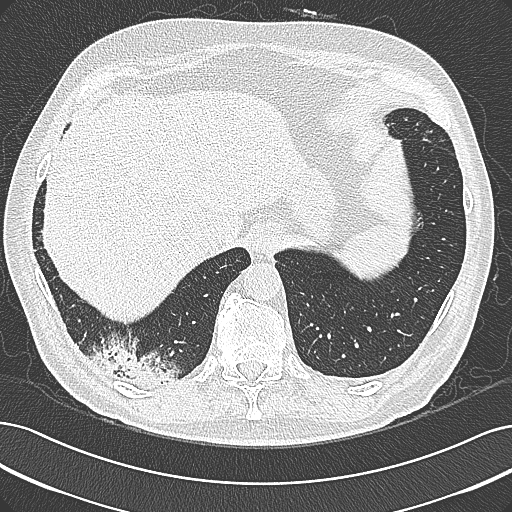
Chest CT (low-dose screening protocol), one axial image. Baseline annual screen. Lung window (W 1500 / L -600 HU). 1 mm slice thickness. Lung (sharp) reconstruction kernel (B80f). 120 kVp. 512 × 512 image matrix, field of view 362 × 362 mm. Male, age 68 years at enrolment. Former smoker at enrolment.
Lesion marked by an expert reader, bounding box (x1, y1, x2, y2) in pixels: (95, 338, 190, 399). No non-calcified nodule or mass ≥4 mm was recorded by the screening reader at this exam. Official screen result: negative screen, significant abnormalities not suspicious for lung cancer. Lung cancer was diagnosed 154 days after this screen: mucinous adenocarcinoma, right lower lobe, well differentiated (G1), stage IB (AJCC 6th edition), 50 mm at pathology.